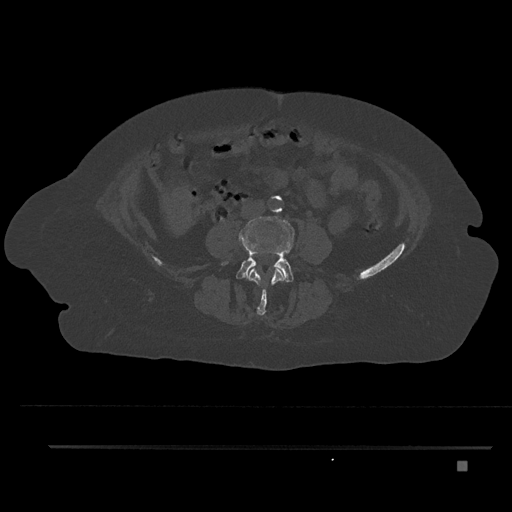
CT including the spine, one axial slice. Slice 97 of 797 in the series (ordered by position). 120 kVp. Bone window (W 1800 / L 400 HU). 512 × 512 image matrix, field of view 437 × 437 mm. Female patient, age 76 years. From the clinical record (not read from this slice): primary cancer: lung.
Structures marked on this image (semi-automatically segmented with operator editing):
- L3 vertebra: bounding box <248,267,285,315> (left, top, right, bottom; pixels)
- L4 vertebra: <222,216,295,283>